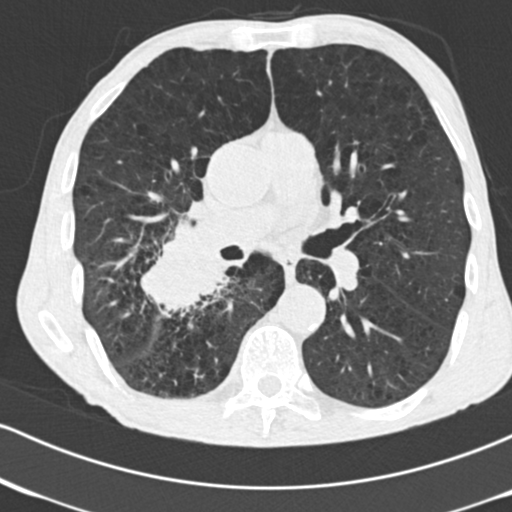
Low-dose screening chest CT, axial slice; second annual screen; lung window (W 1500 / L -600 HU); 2 mm slice thickness; 512 × 512 image matrix. Male, age 64 years at enrolment. Current smoker at enrolment.
Lesion marked by an expert reader, bounding box (x1, y1, x2, y2) in pixels: (131, 230, 239, 329). Reader record for this screening exam (exam-level; its link to the box is not recorded): non-calcified nodule or mass ≥4 mm, 52 × 37 mm, spiculated (stellate) margins, soft tissue attenuation, pre-existing on the prior screen: no. Official screen result: positive, other. Lung cancer was diagnosed 28 days after this screen: adenocarcinoma, NOS, right lower lobe, stage IV (AJCC 6th edition), 60 mm at pathology.